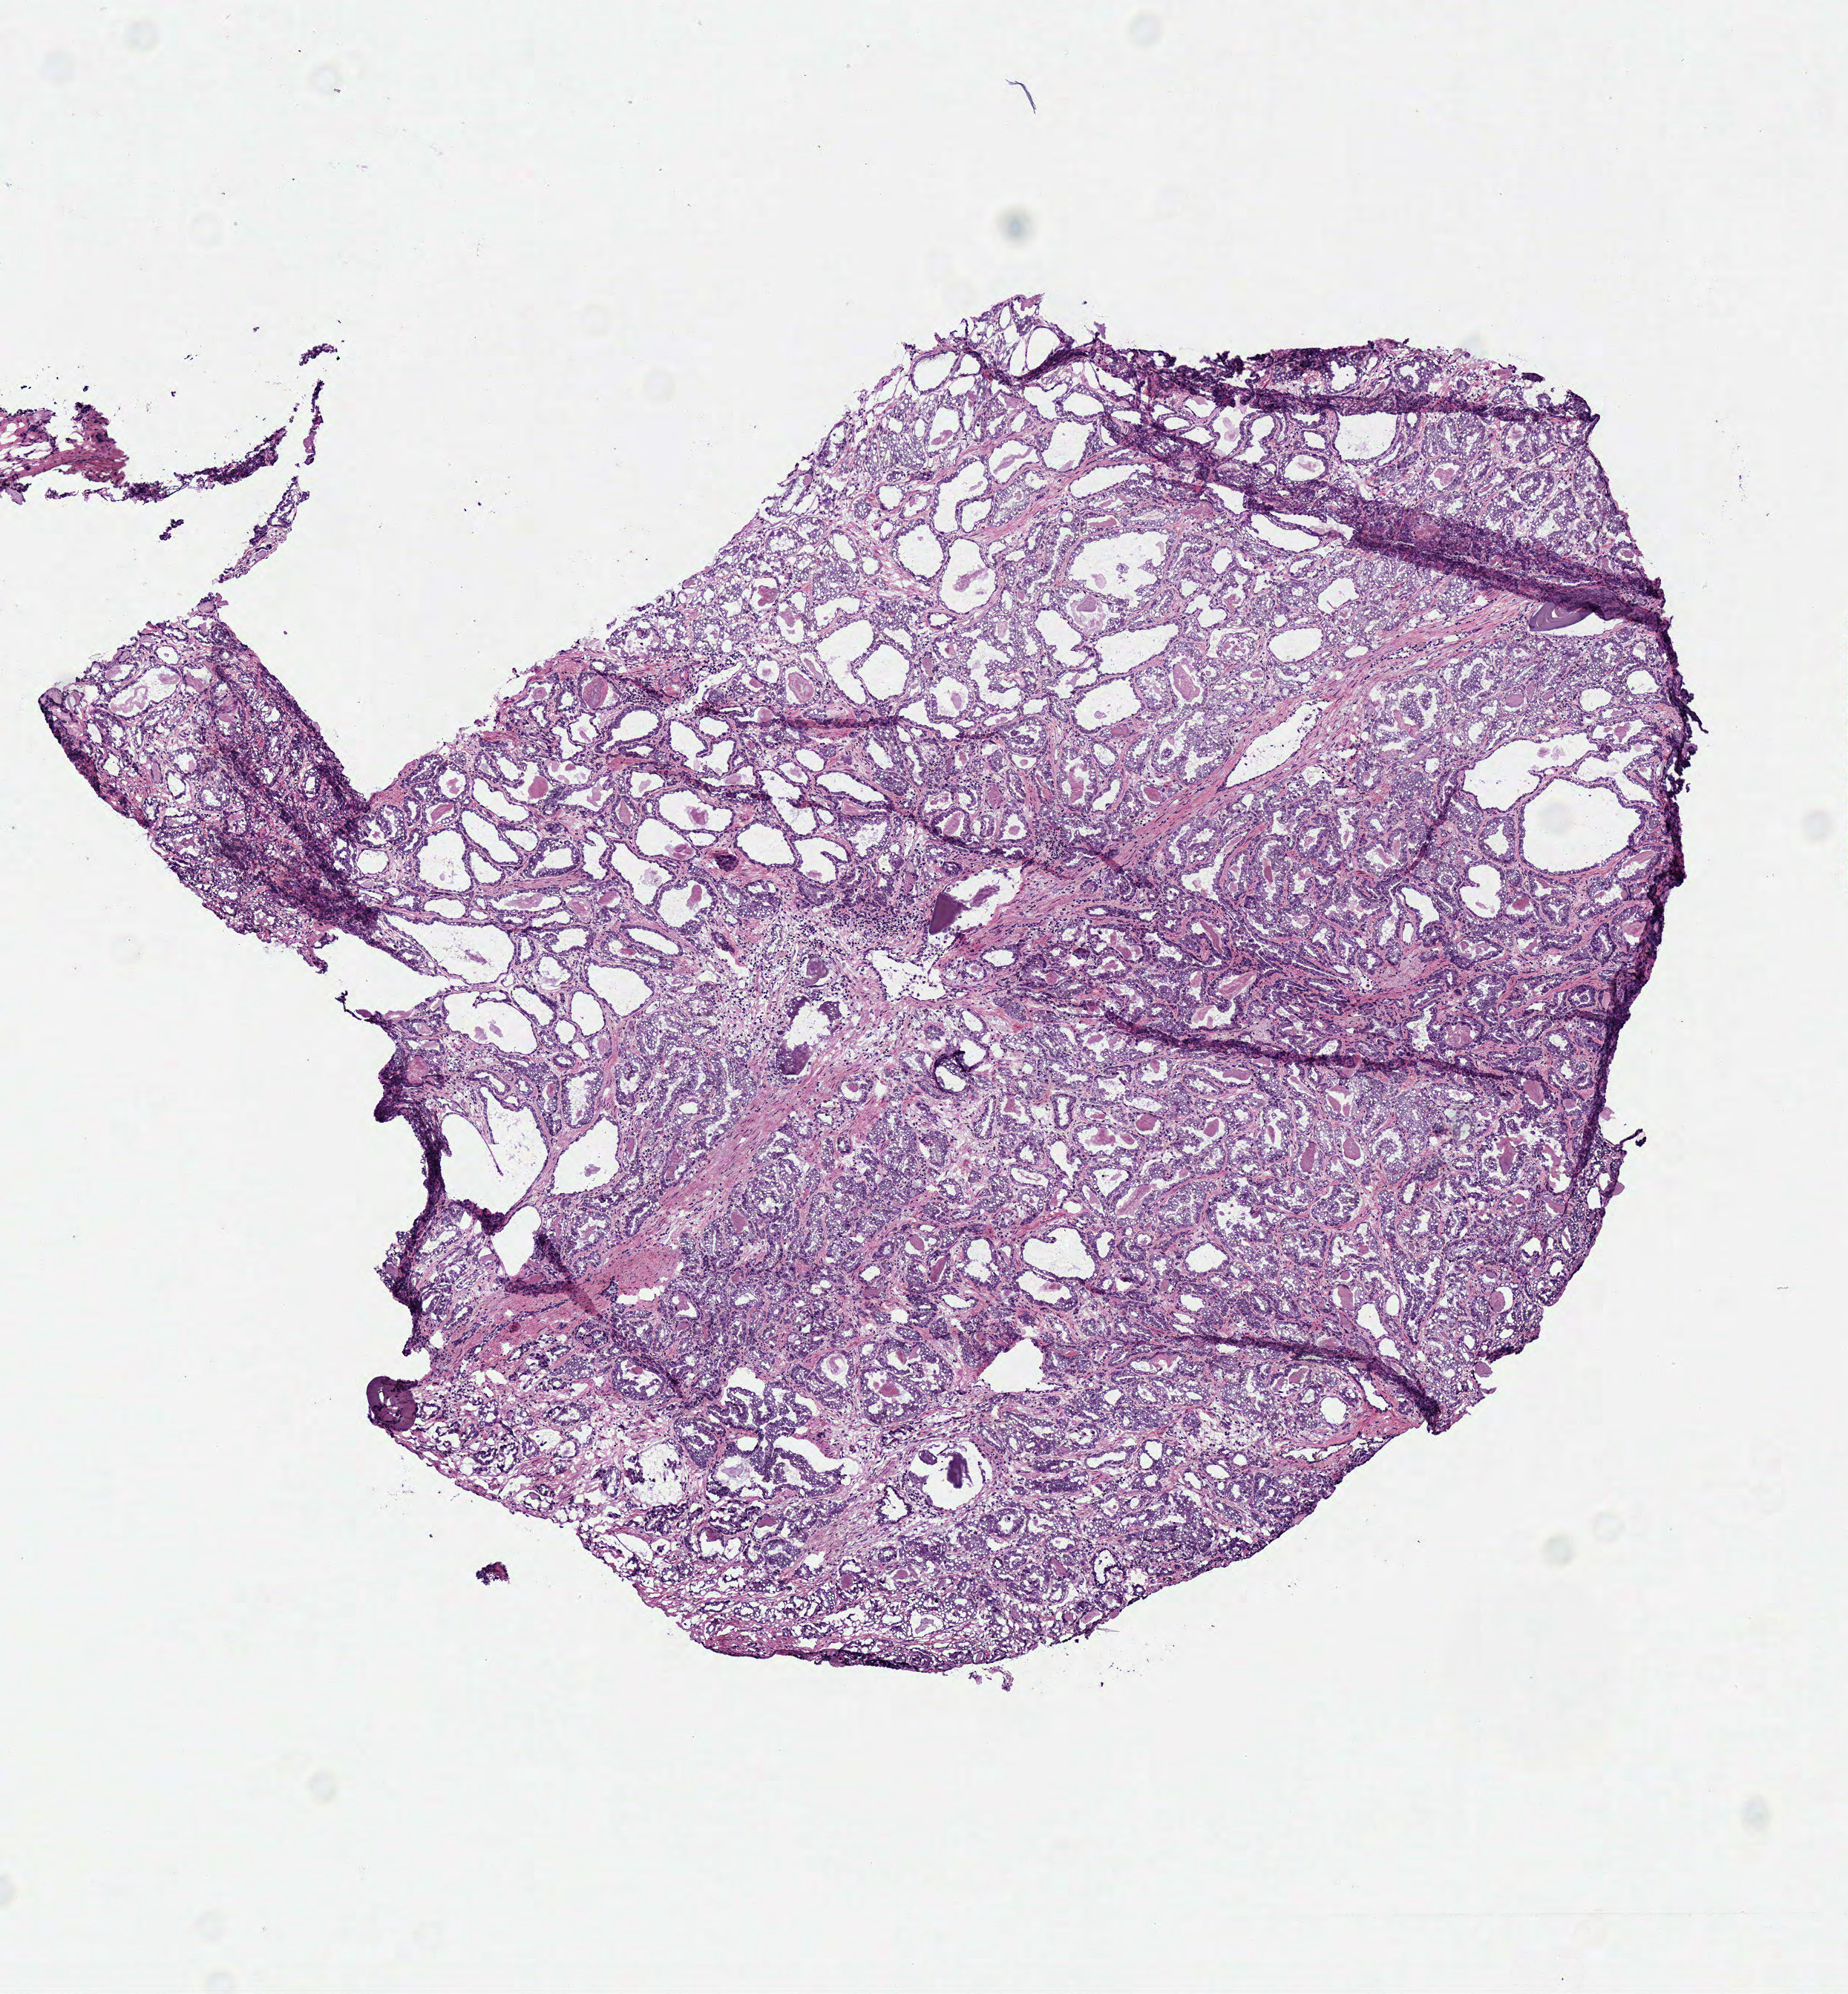
Digitized H&E tissue section (whole slide), shown as a low-resolution overview of the whole scanned area (about 4.9 x 5.3 mm, from a 40x scan), frozen section from the top of the tissue portion, sample: primary tumour, prostate. Patient: male, age at initial diagnosis 55 years. Gleason score: 7 (4+3). Pathologist review of this section (percent, as recorded): tumour cells 70%, tumour nuclei 75%, normal cells 15%, stromal cells 10%, necrosis 0%. Inflammatory infiltration, as recorded: lymphocyte infiltration 1%, monocyte infiltration 0%, neutrophil infiltration 0%.
Laterality: bilateral. Diagnosis: Acinar cell carcinoma (prostate gland). Lymph nodes positive (case pathology): 0 of 7 examined.